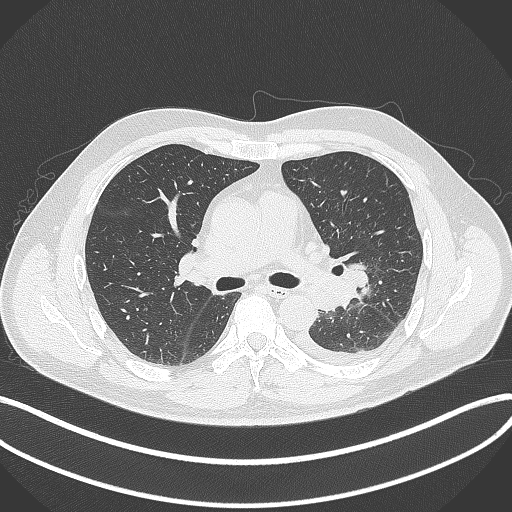
Chest CT, one axial slice; position 217 of 342 along the scan axis; reconstruction kernel B70f; lung window (W 1500 / L -600 HU); 1 mm slice thickness; 512 × 512 image matrix, field of view 400 × 400 mm. Patient: male, 58 years. From the clinical record (not read from this slice): clinical TNM (as recorded): T3 N1 M1b.
Outlined on this slice (rectangle marked by the reading radiologist):
- lung tumour (recorded histology: small cell carcinoma): bounding box [x1, y1, x2, y2] px = [337, 262, 371, 292]